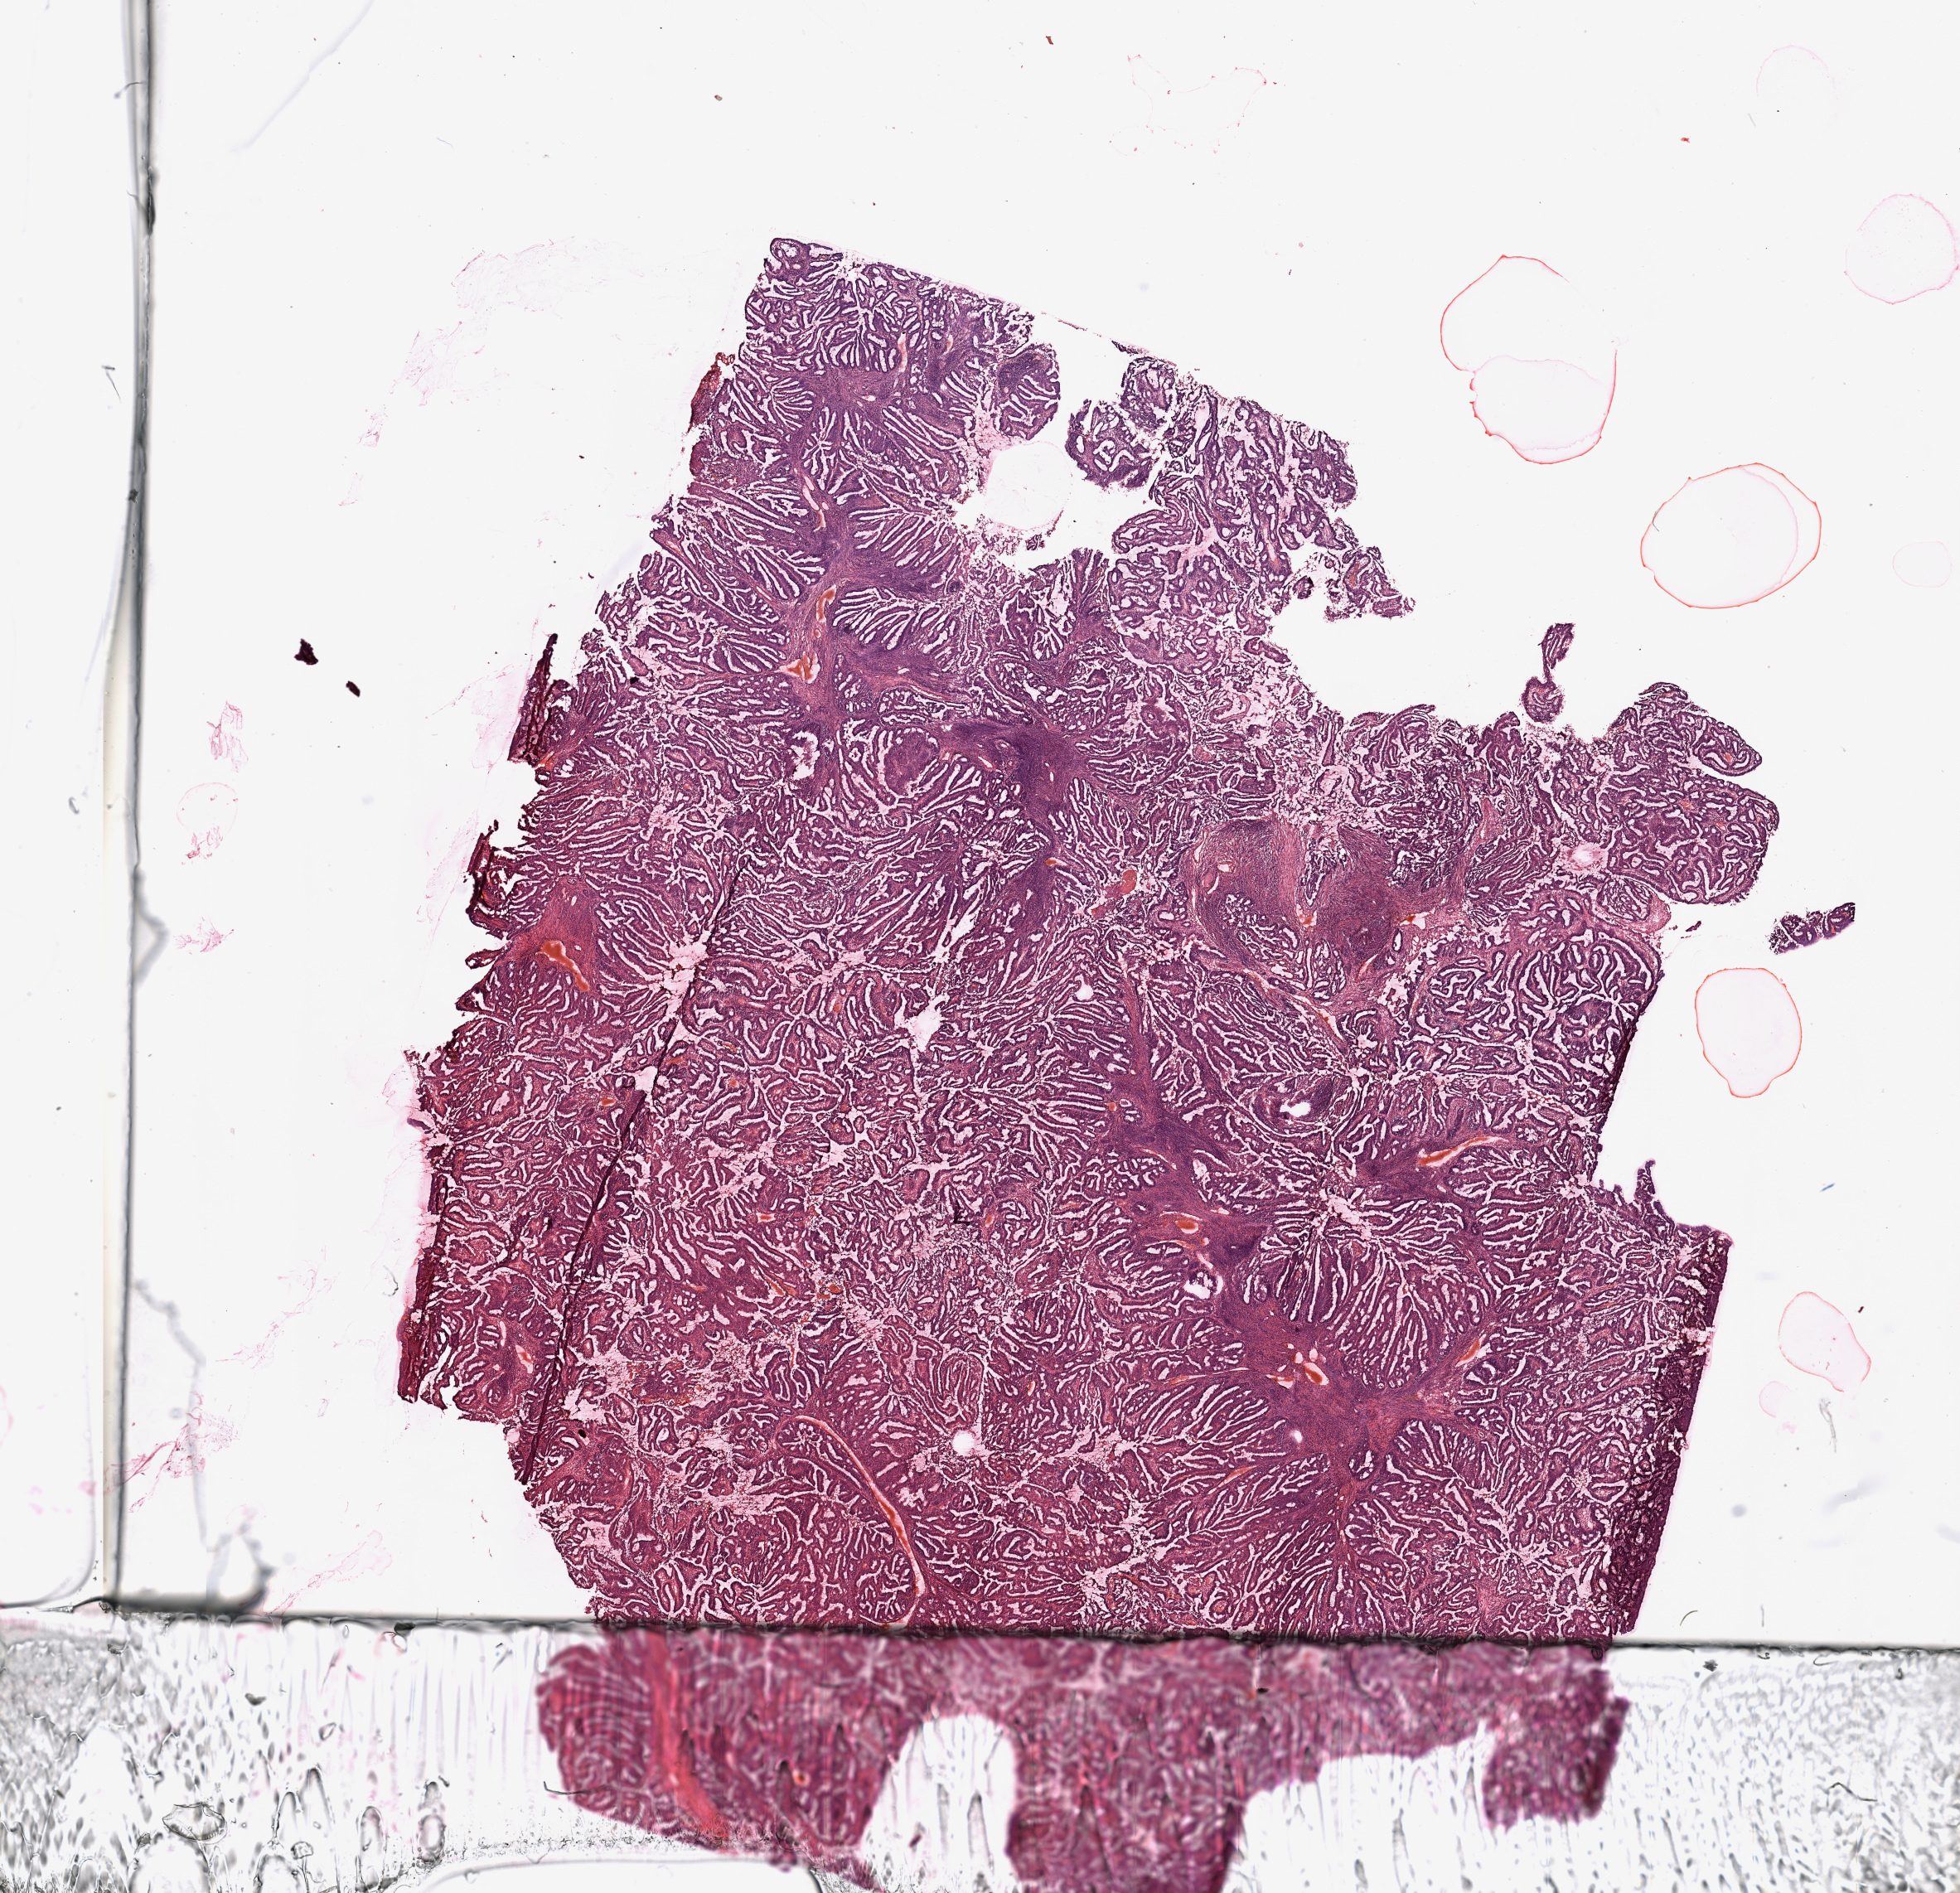
Digitized Hematoxylin and eosin (H&E) stained tissue section (whole slide) — a low-resolution overview of the entire scanned area, about 18.7 x 18.1 mm (from a 20x scan); tumour tissue sample, uterus. 65-year-old female patient. Histologic grade: G2 (moderately differentiated).
* AJCC pathologic stage: III
* diagnosis: Endometrioid adenocarcinoma, NOS